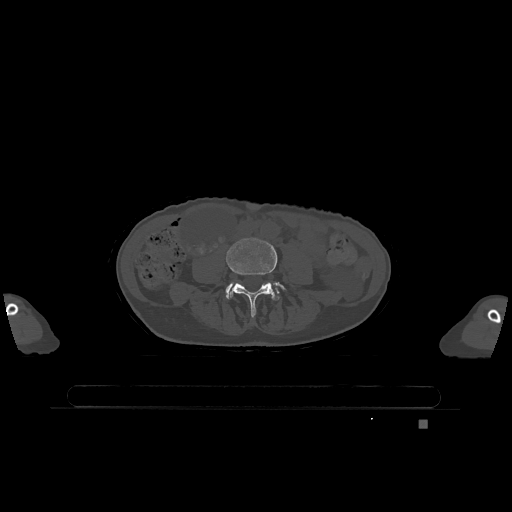
CT including the spine, one axial slice; slice 291 of 1317 in the series (ordered by position); bone window (W 1800 / L 400 HU); 512 × 512 image matrix, field of view 500 × 500 mm. Female patient, age 74 years. From the clinical record (not read from this slice): primary cancer: lung.
Annotated regions visible in this slice (semi-automatic segmentation, software-assisted and operator-edited):
- L4 vertebra: box from (x=226, y=238) to (x=286, y=317) px
- L5 vertebra: (x=226, y=284)–(x=279, y=299)